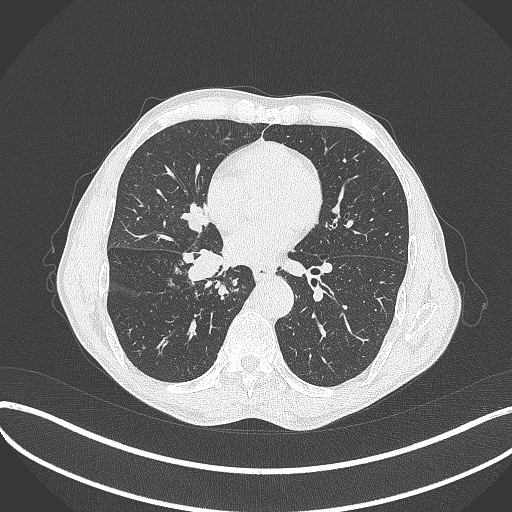
Chest CT, one axial slice; slice 195 of 481 in the series (ordered by position); reconstruction kernel B70f; 120 kVp; lung window (W 1500 / L -600 HU); 1 mm slice thickness; 512 × 512 image matrix. Patient: male, 65 years. Case-level facts recorded for this patient, not image findings: clinical TNM (as recorded): T2a N0 M0.
Structures marked on this image (rectangle marked by the reading radiologist):
- lung tumour (recorded histology: squamous cell carcinoma): bounding box [x1, y1, x2, y2] px = [175, 246, 228, 290]